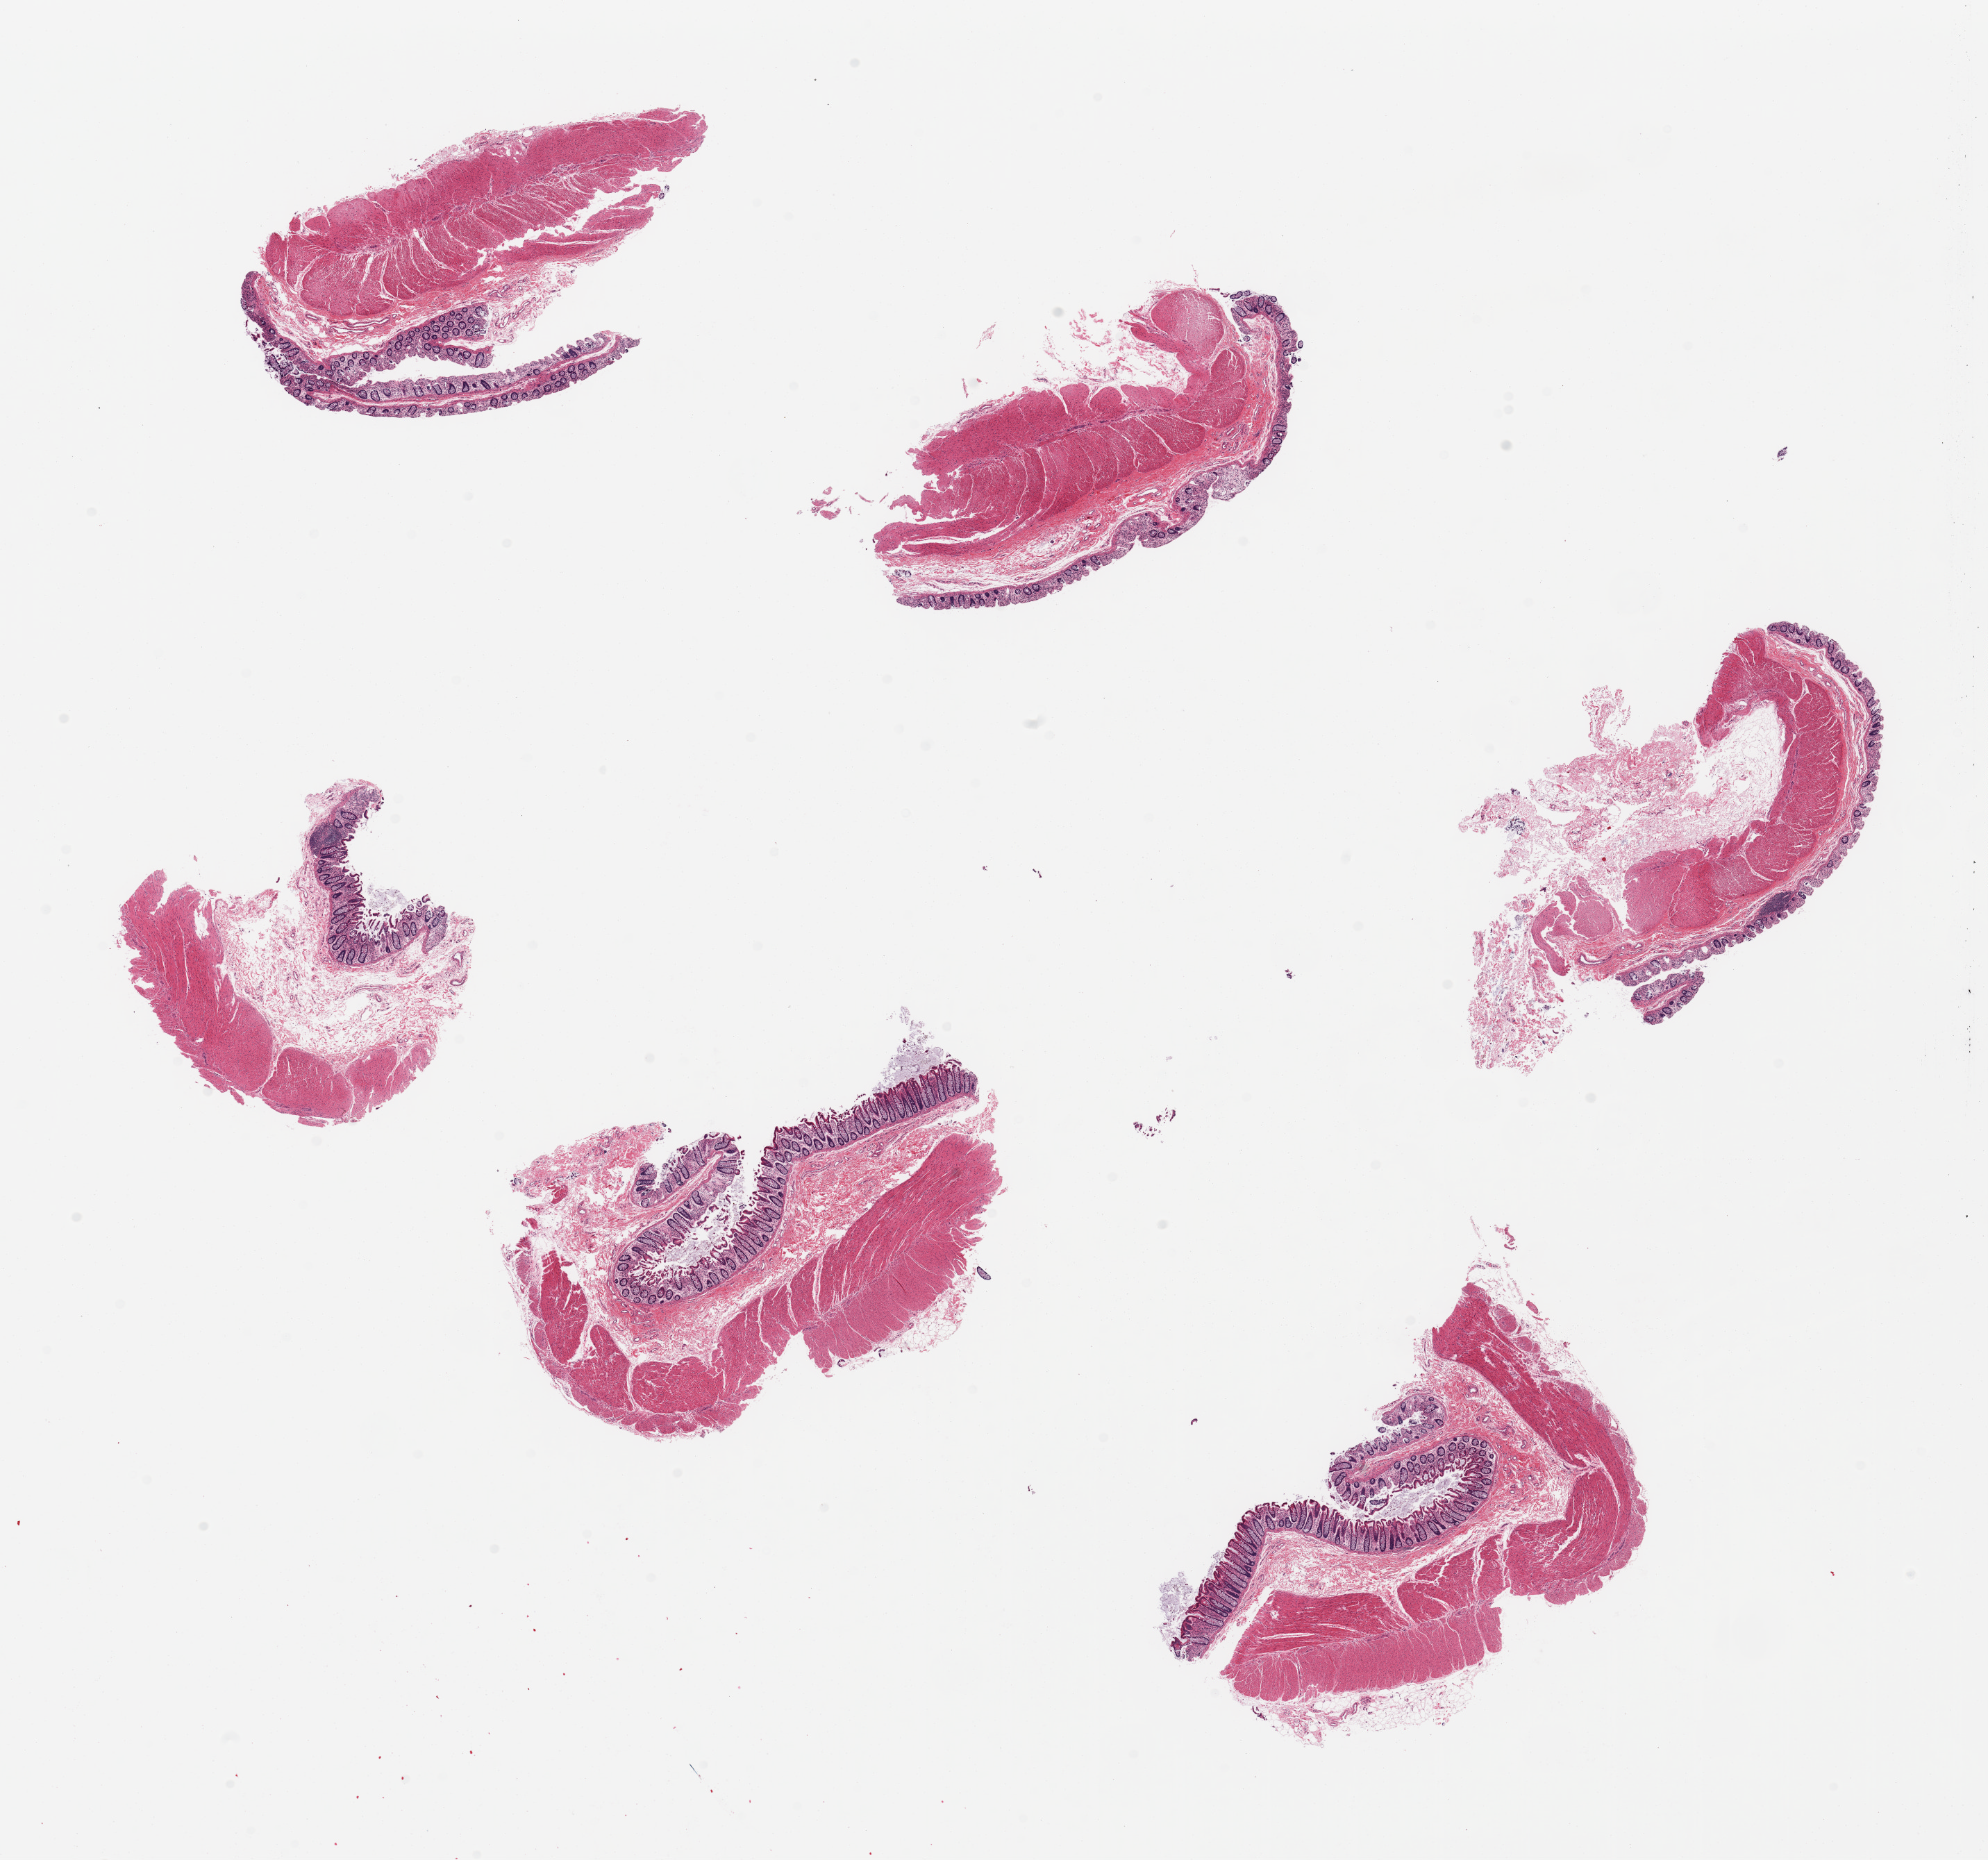
Digitized haematoxylin and eosin-stained section, brightfield, a low-resolution overview of the entire scanned area, about 22.6 x 21.2 mm (from a 20x scan), PAXgene-fixed paraffin-embedded (PFPE) section, sampled site (target tissue): transverse colon, donor tissue sample.
Review note (as recorded): 6 pieces, mucosa score ranges from 1 to mainly '2' as noted; ~15% total thickness, ~0.5mm.